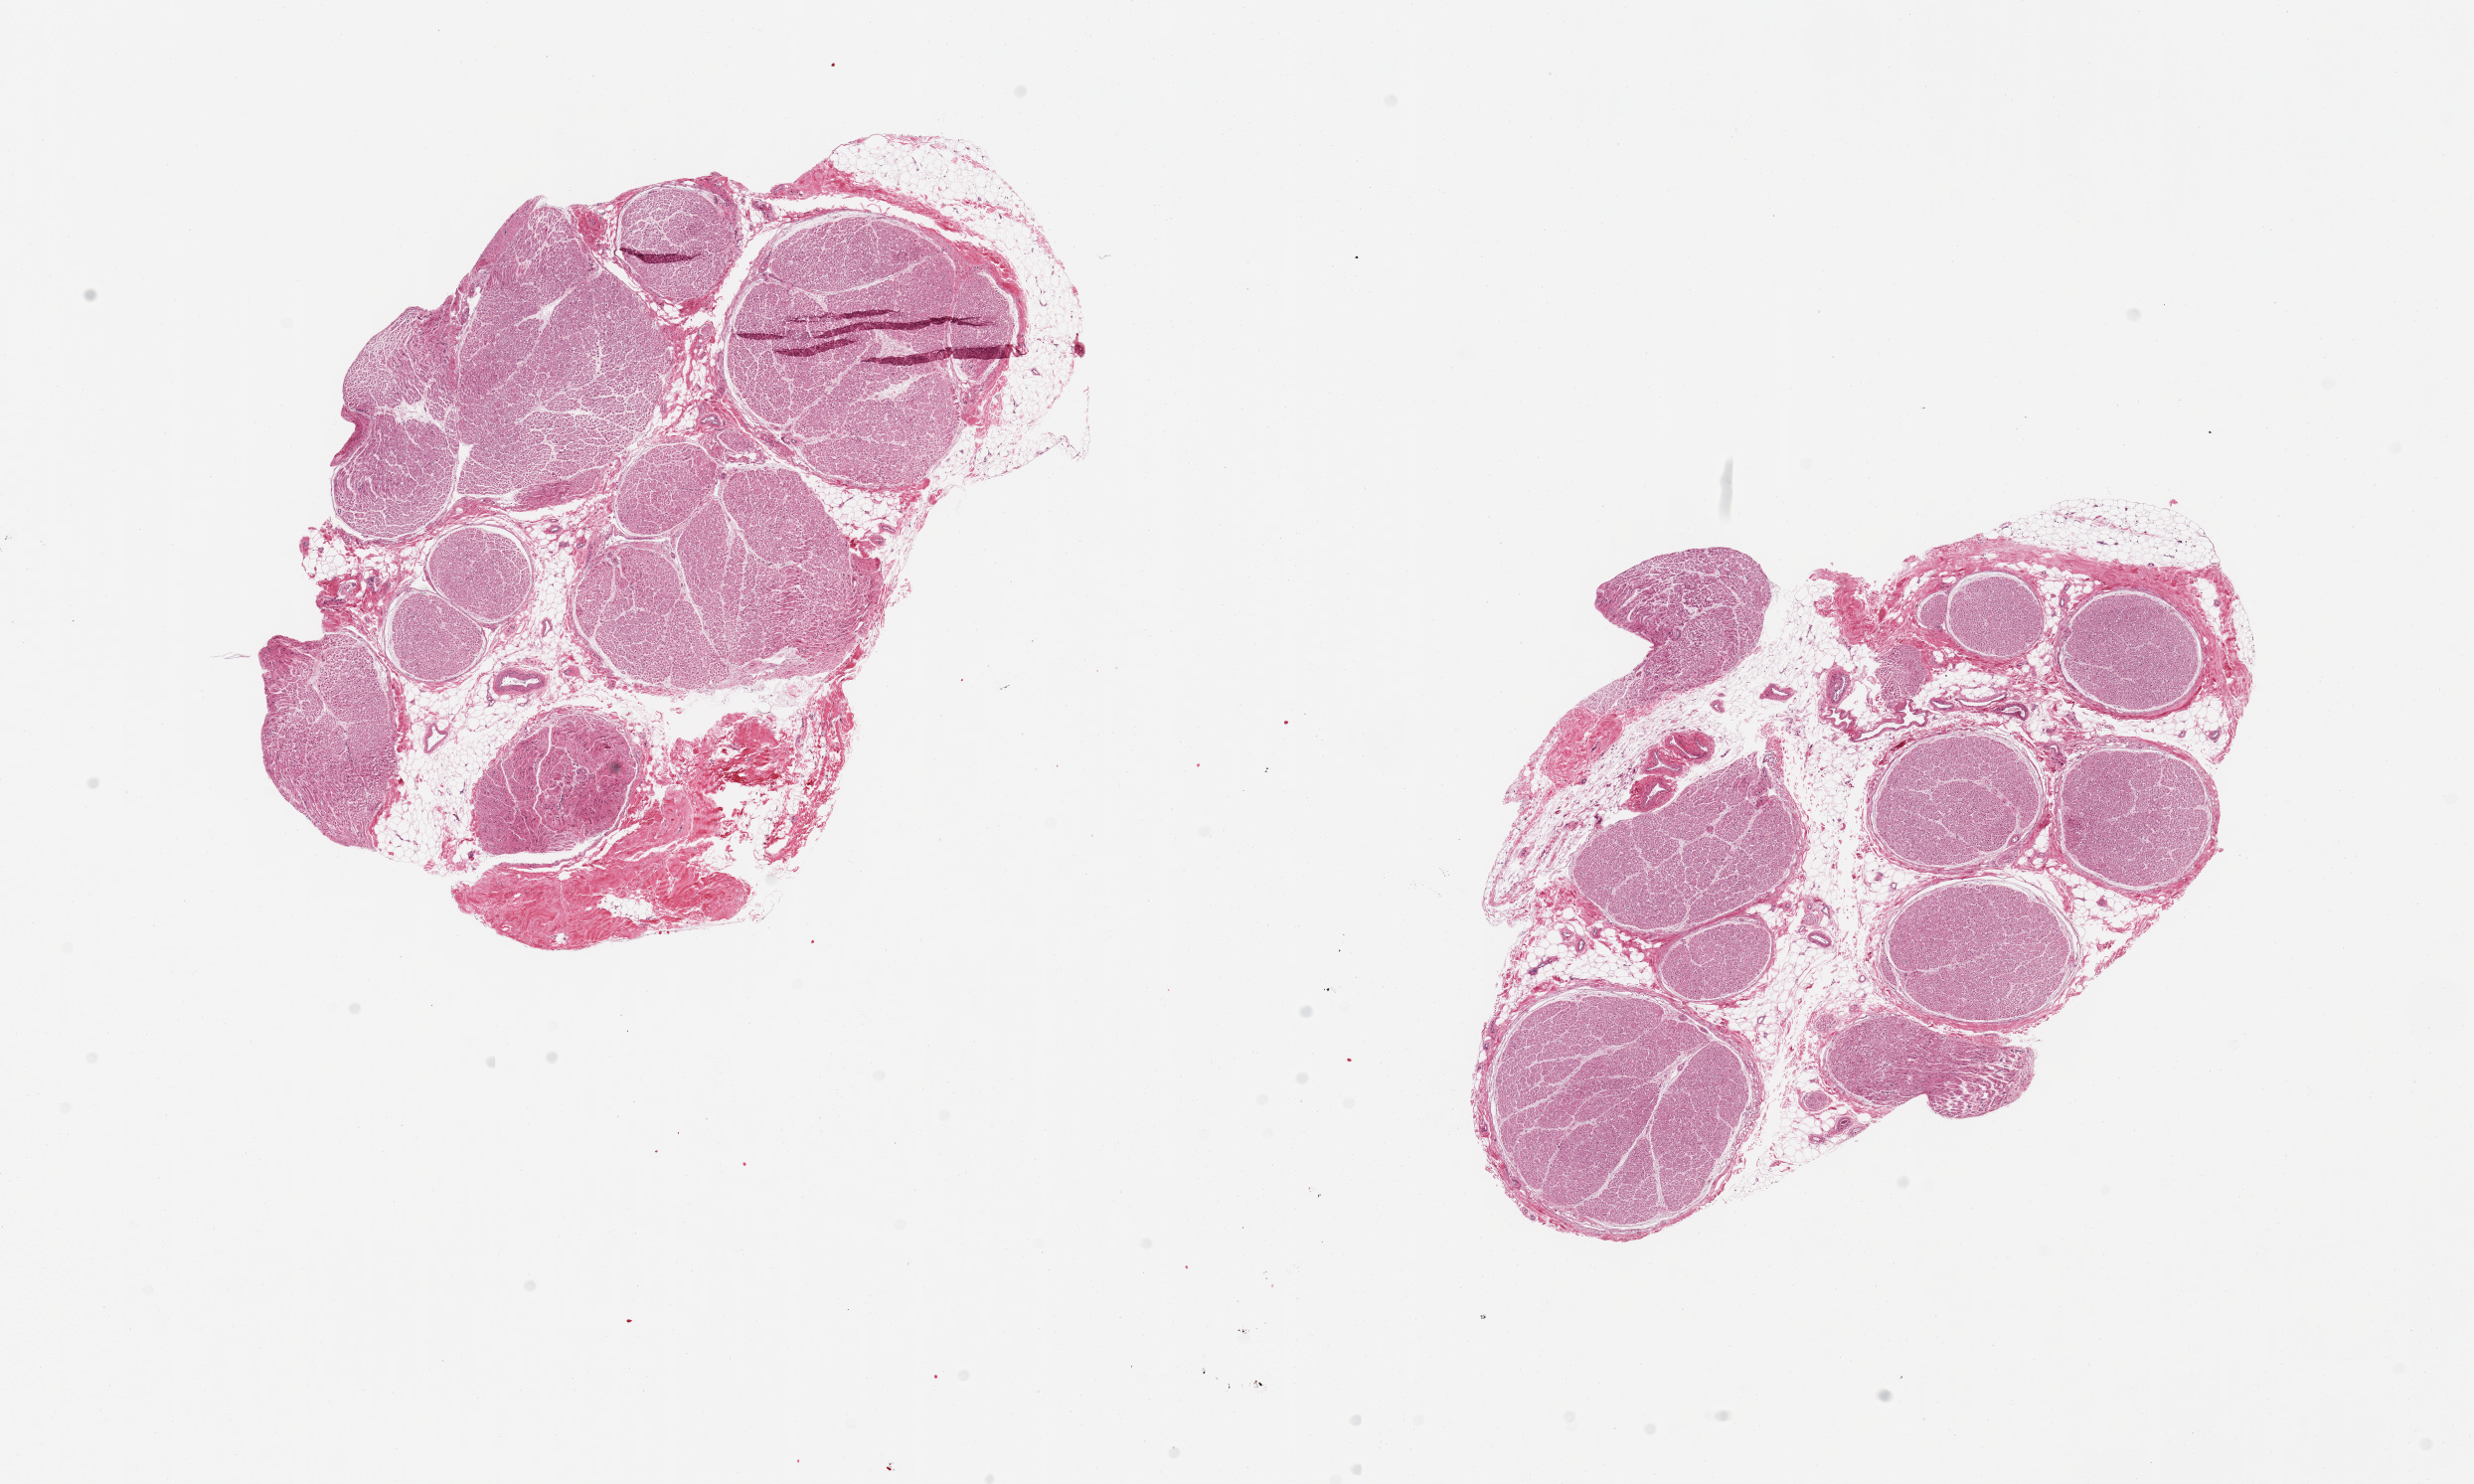
Digitized haematoxylin and eosin-stained section, brightfield — a low-resolution overview of the entire scanned area, about 19.7 x 11.8 mm (acquisition: 20x scan), PAXgene-fixed, paraffin-embedded tissue, sampled site (target tissue): tibial nerve, donor tissue sample. Donor sex: male.
Reviewer comment on this tissue sample: 2 pieces, clean, minimal adherent fat, minute ~0.5mm nubbin.